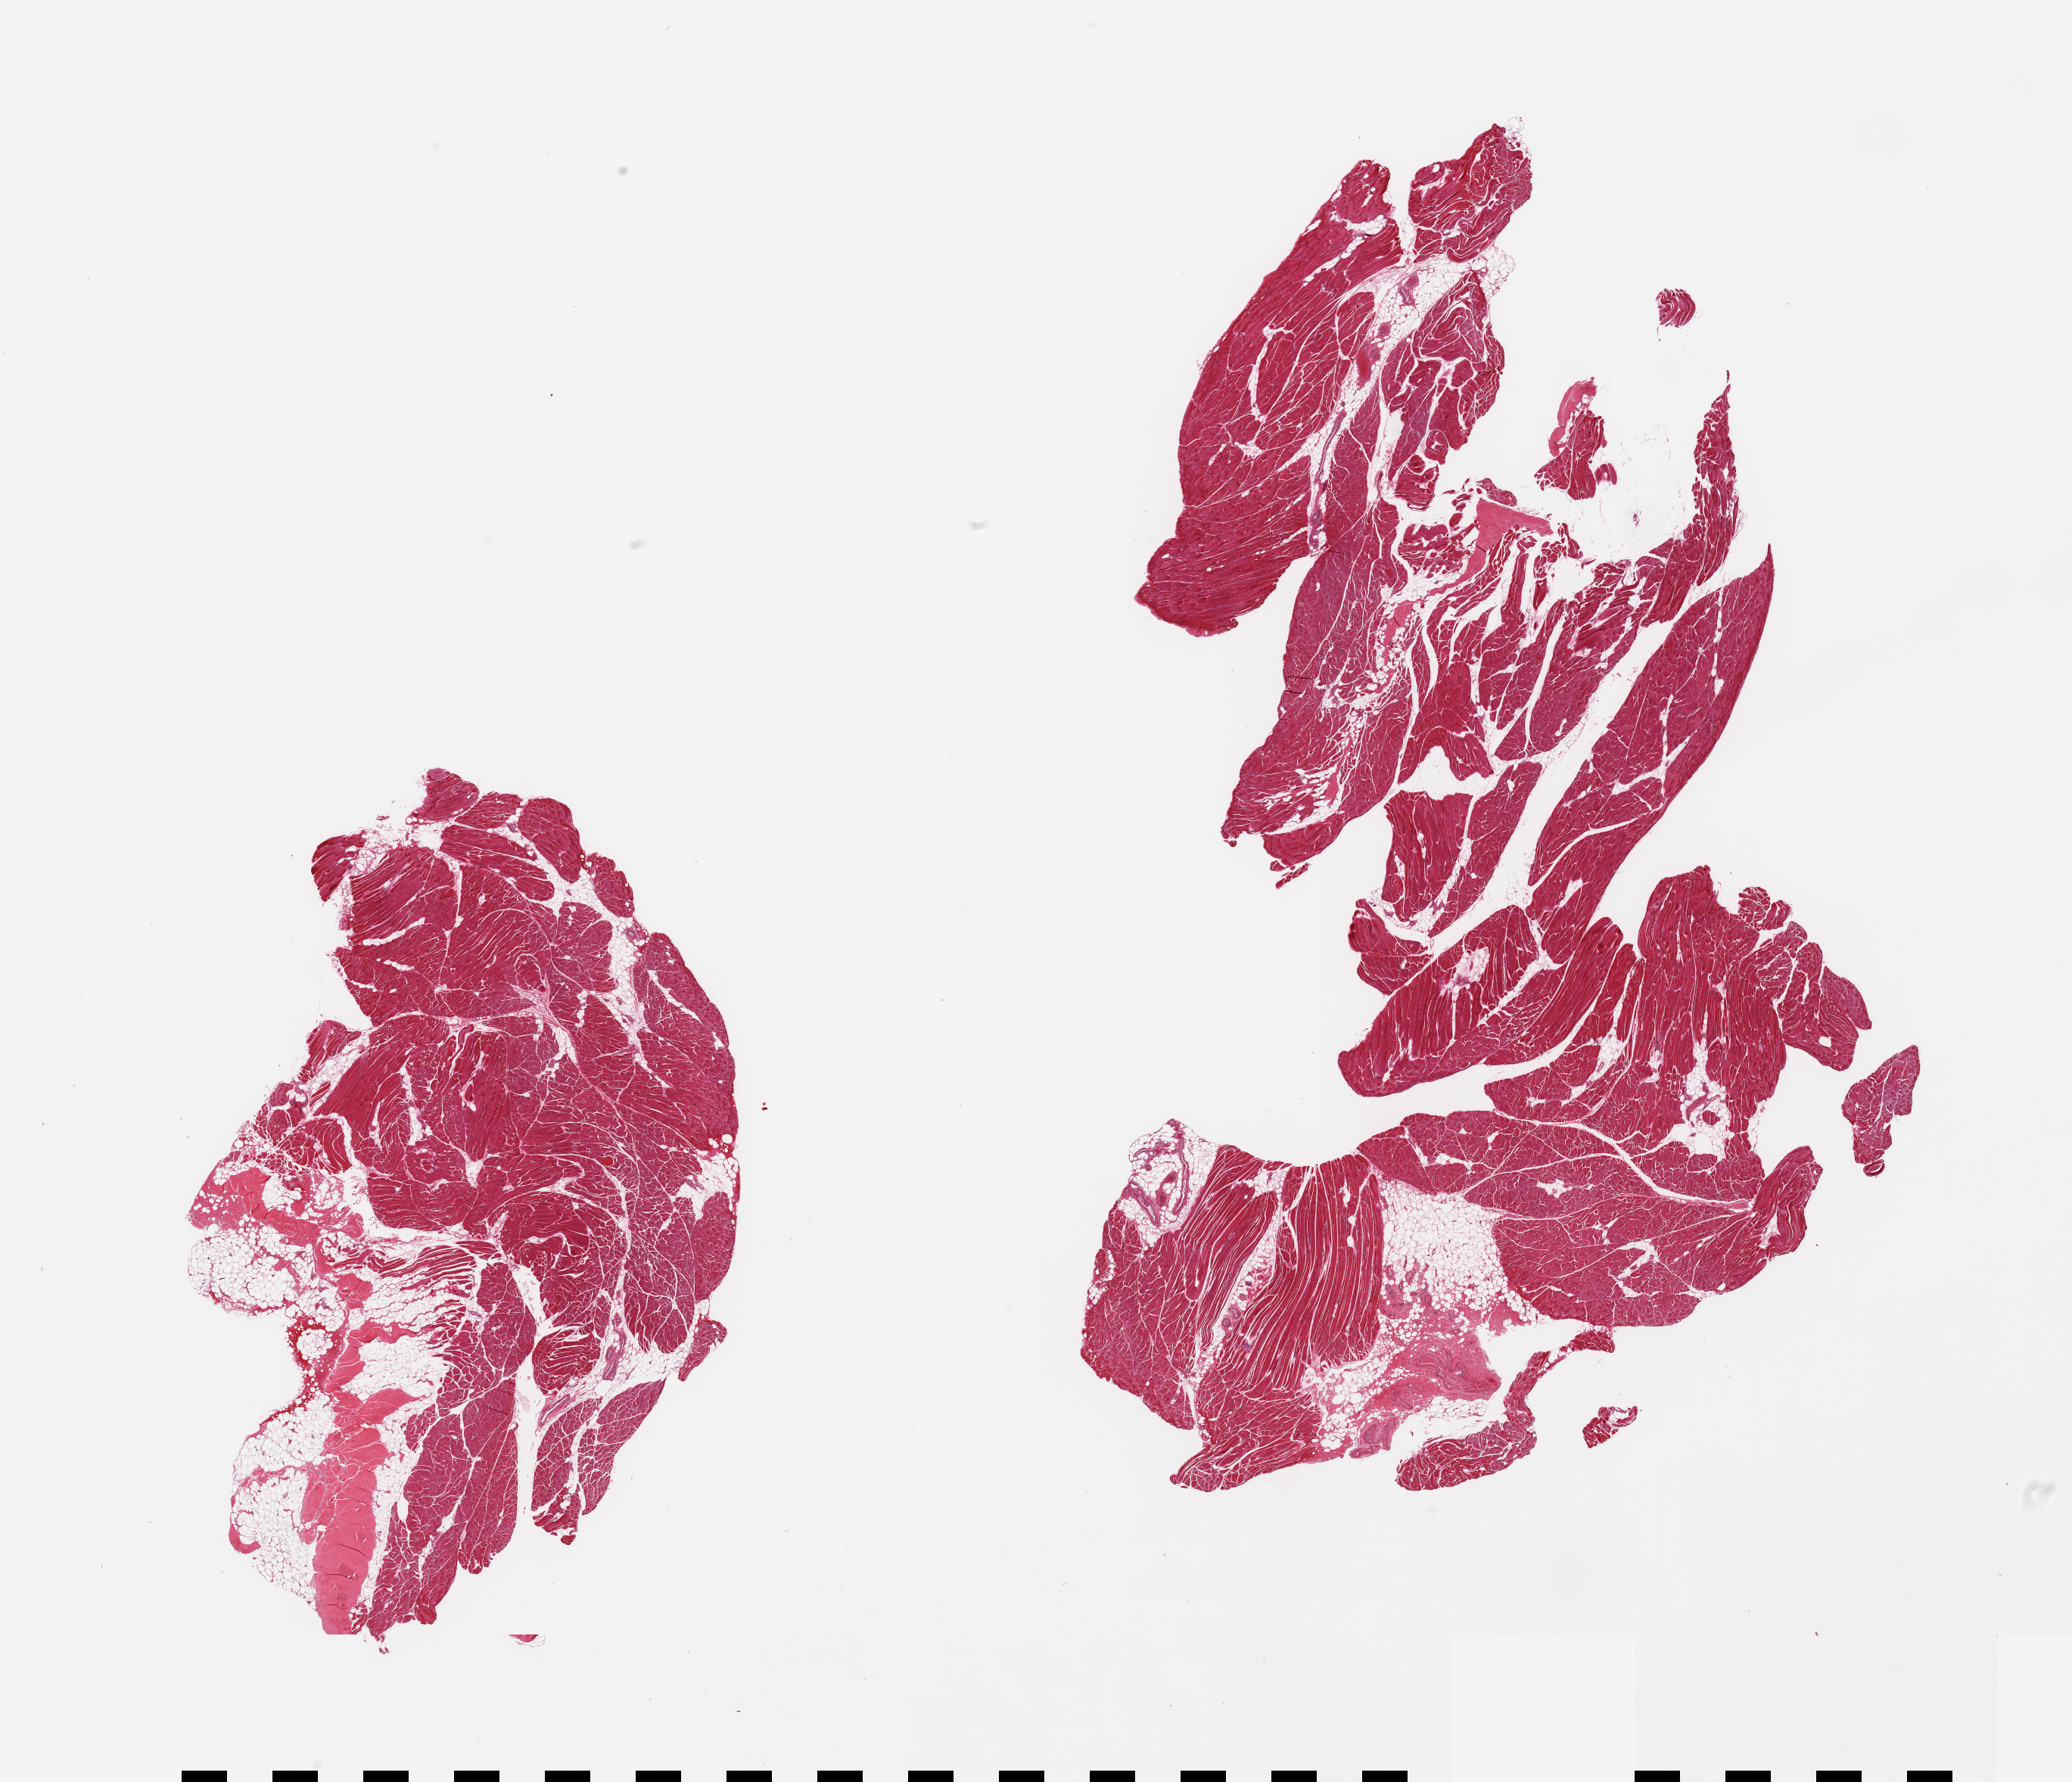
Haematoxylin and eosin whole-slide image, whole scanned area (about 21.7 x 18.6 mm, acquisition: 20x scan) shown as a low-resolution overview. PAXgene-fixed paraffin-embedded (PFPE) section. Section of skeletal muscle (target tissue). Donor tissue sample. Donor: female.
Reviewer comment on this tissue sample: 2 pieces; 10% internal fat; tendon in 1 piece, 10% area.